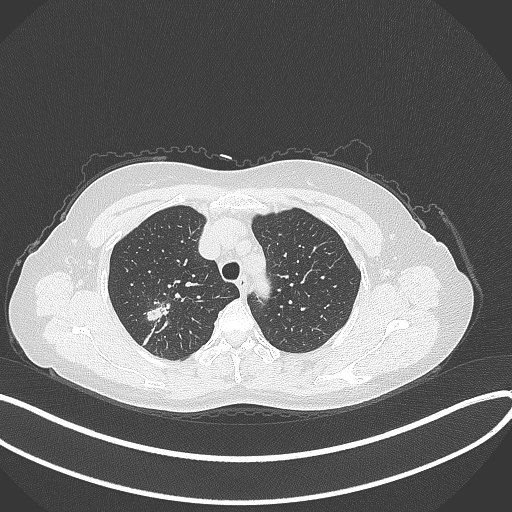
Chest CT, one axial slice. Slice 286 of 337 in the series (ordered by position). 120 kVp. Lung window (W 1500 / L -600 HU). 1 mm slice thickness. 512 × 512 image matrix. Patient: female, 50 years. Case-level facts recorded for this patient, not image findings: clinical TNM (as recorded): T1c N0 M0.
Outlined on this slice (rectangle marked by the reading radiologist):
- lung tumour (recorded histology: adenocarcinoma): bounding box (x1, y1, x2, y2) in pixels: (134, 298, 179, 325)